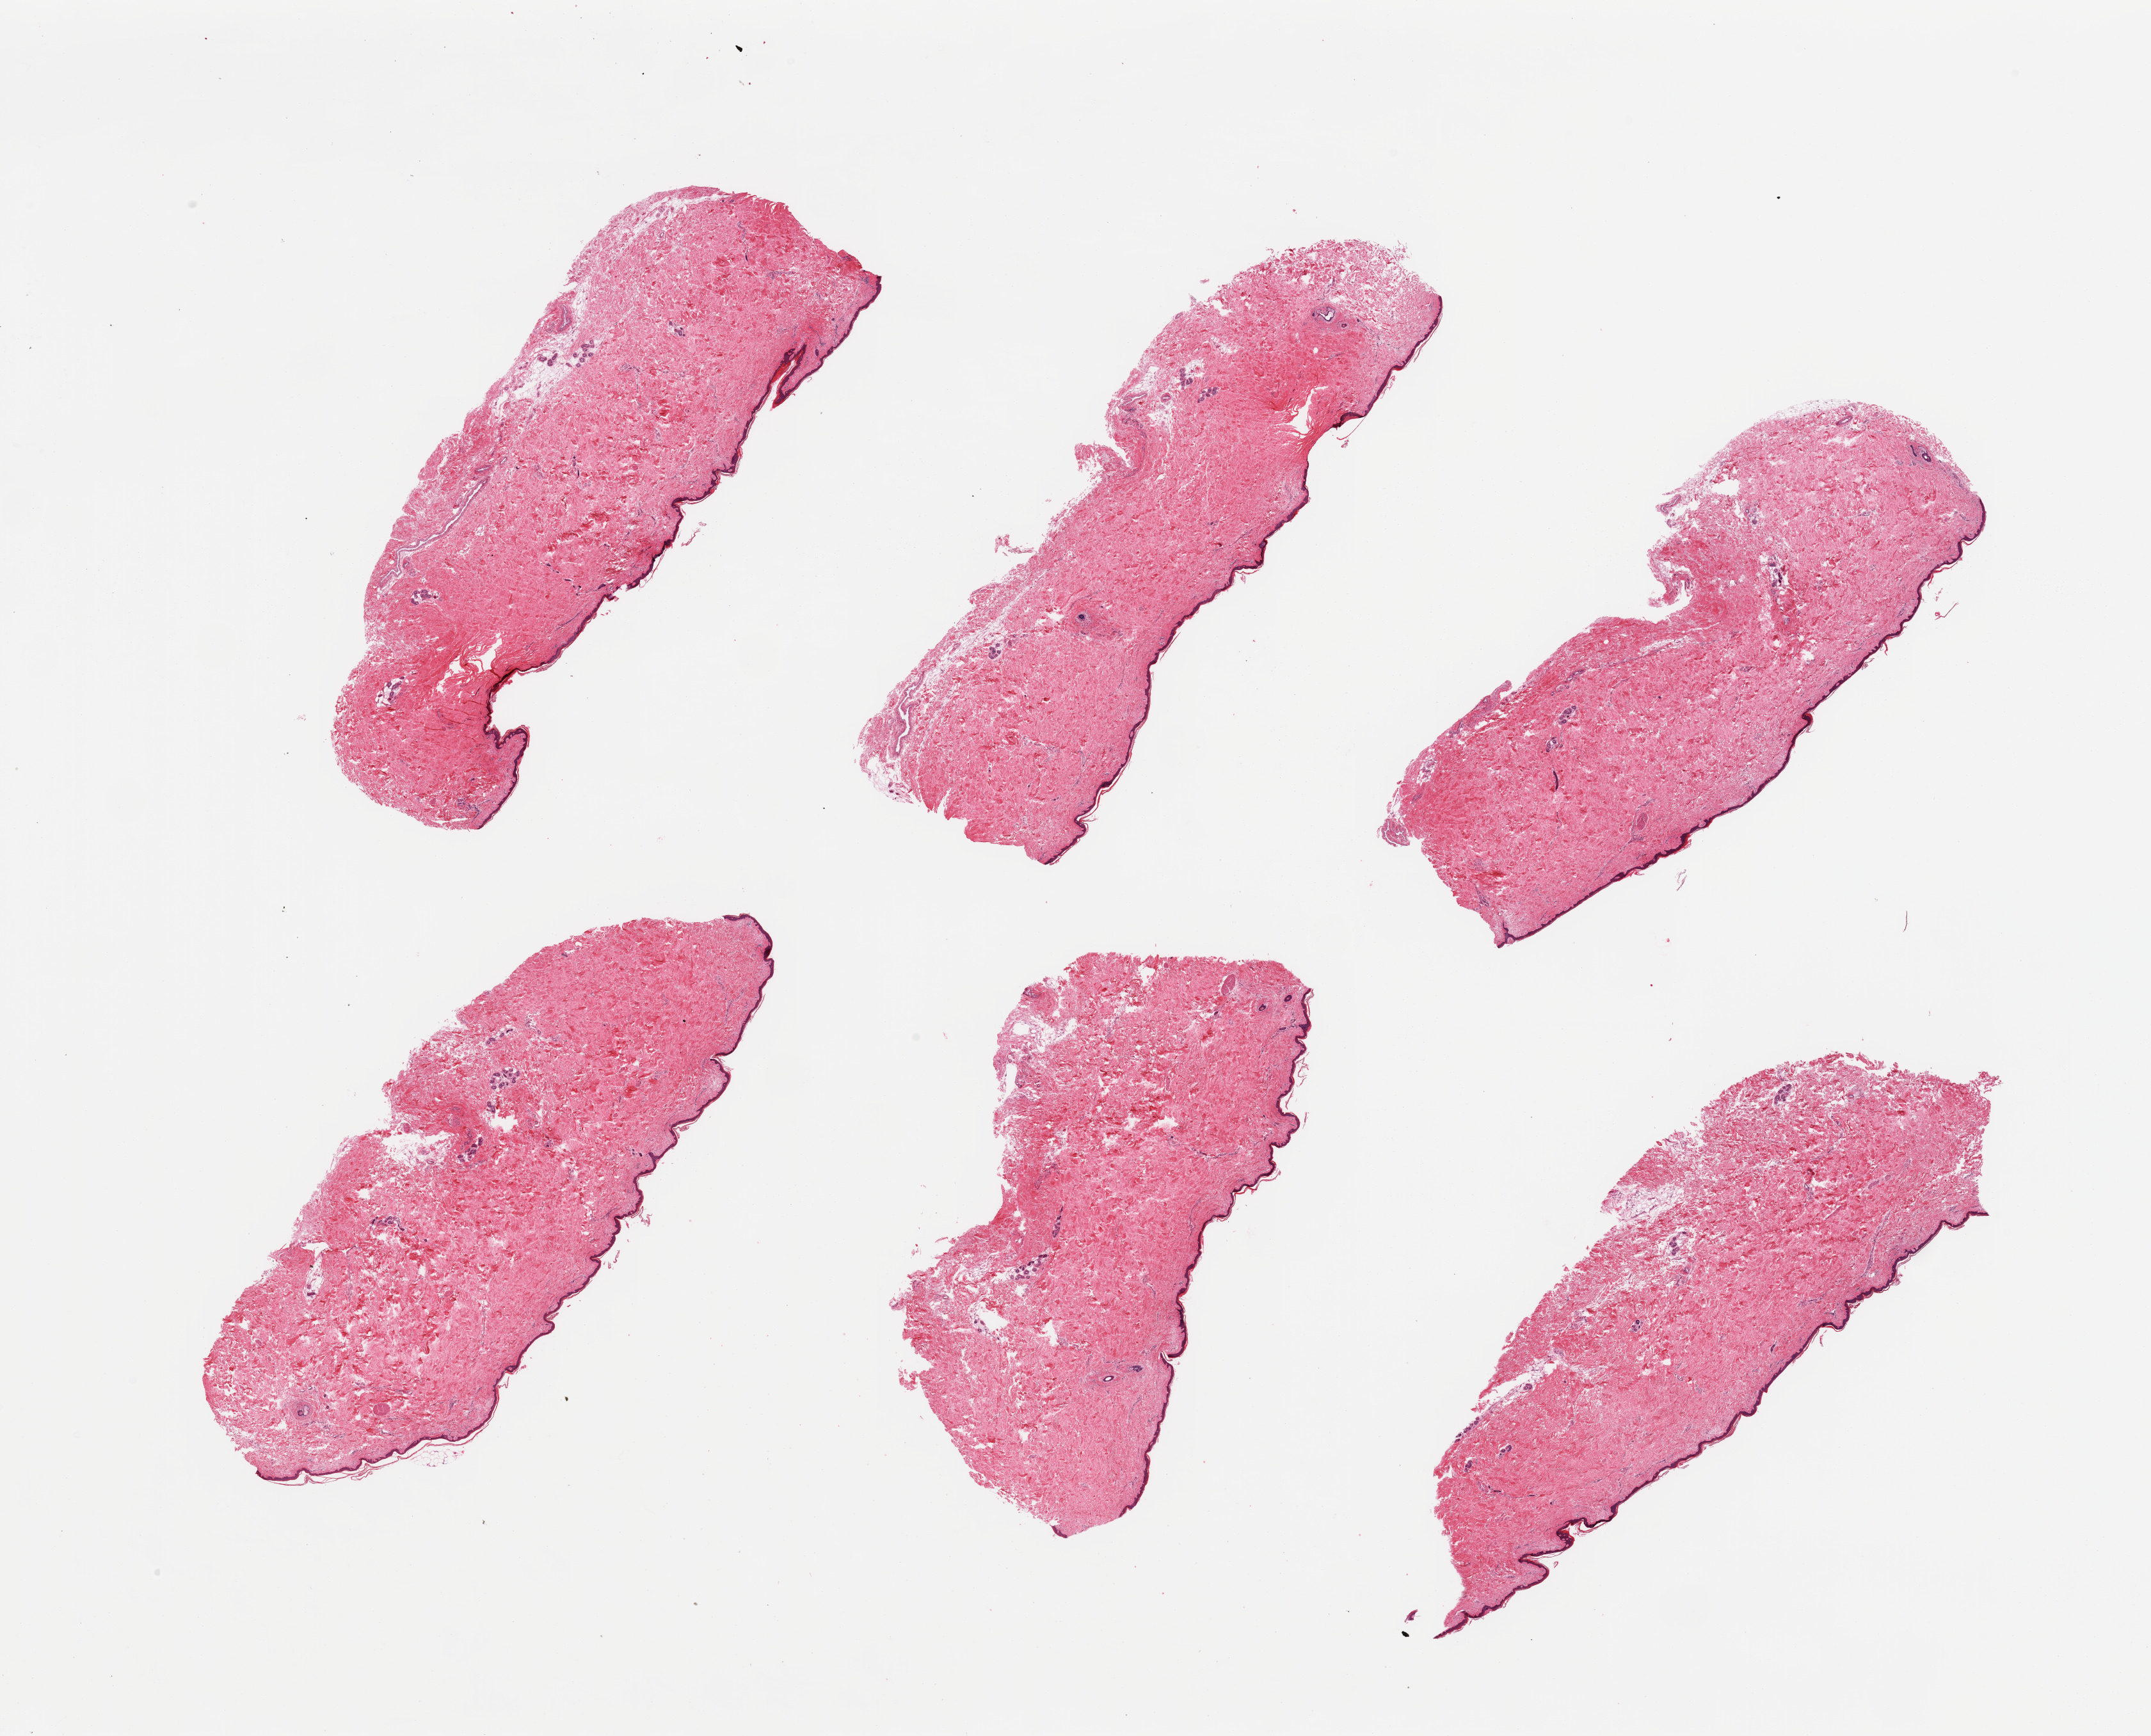
Hematoxylin and eosin (H&E) whole-slide image, brightfield — whole scanned area (about 26.6 x 21.5 mm, acquisition: 20x scan) shown as a low-resolution overview; PAXgene-fixed, paraffin-embedded tissue; target tissue: skin of suprapubic region; donor tissue sample. Donor: male.
- review note (as recorded): 6 pieces; well trimmed; <5% dermal fat